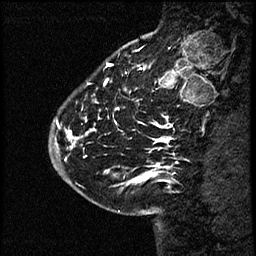
Breast MRI (dynamic contrast-enhanced), one sagittal slice. Slice 16 of 60 in the series (ordered by position). Dynamic contrast-enhanced study with each time point stored as its own series, time point 2 of 4 at this slice position (early post-contrast, ordered by acquisition time). 1.5 T. TE 4.2 ms, TR 17.6 ms. 2 mm slice thickness. 256 × 256 image matrix, field of view 200 × 200 mm. Patient: female, 43 years. Case-level facts recorded for this patient, not image findings: setting: breast cancer imaged before/during neoadjuvant chemotherapy.
Outlined on this slice (semi-automatically segmented with operator editing):
- analysis volume of interest (the breast-tissue region the enhancement analysis was run in; not a lesion): bounding box (x1, y1, x2, y2) in pixels: (54, 56, 169, 191)
- tumour enhancement mask (voxels above the 100 % enhancement threshold inside the analysis volume of interest): (54, 124, 169, 182)